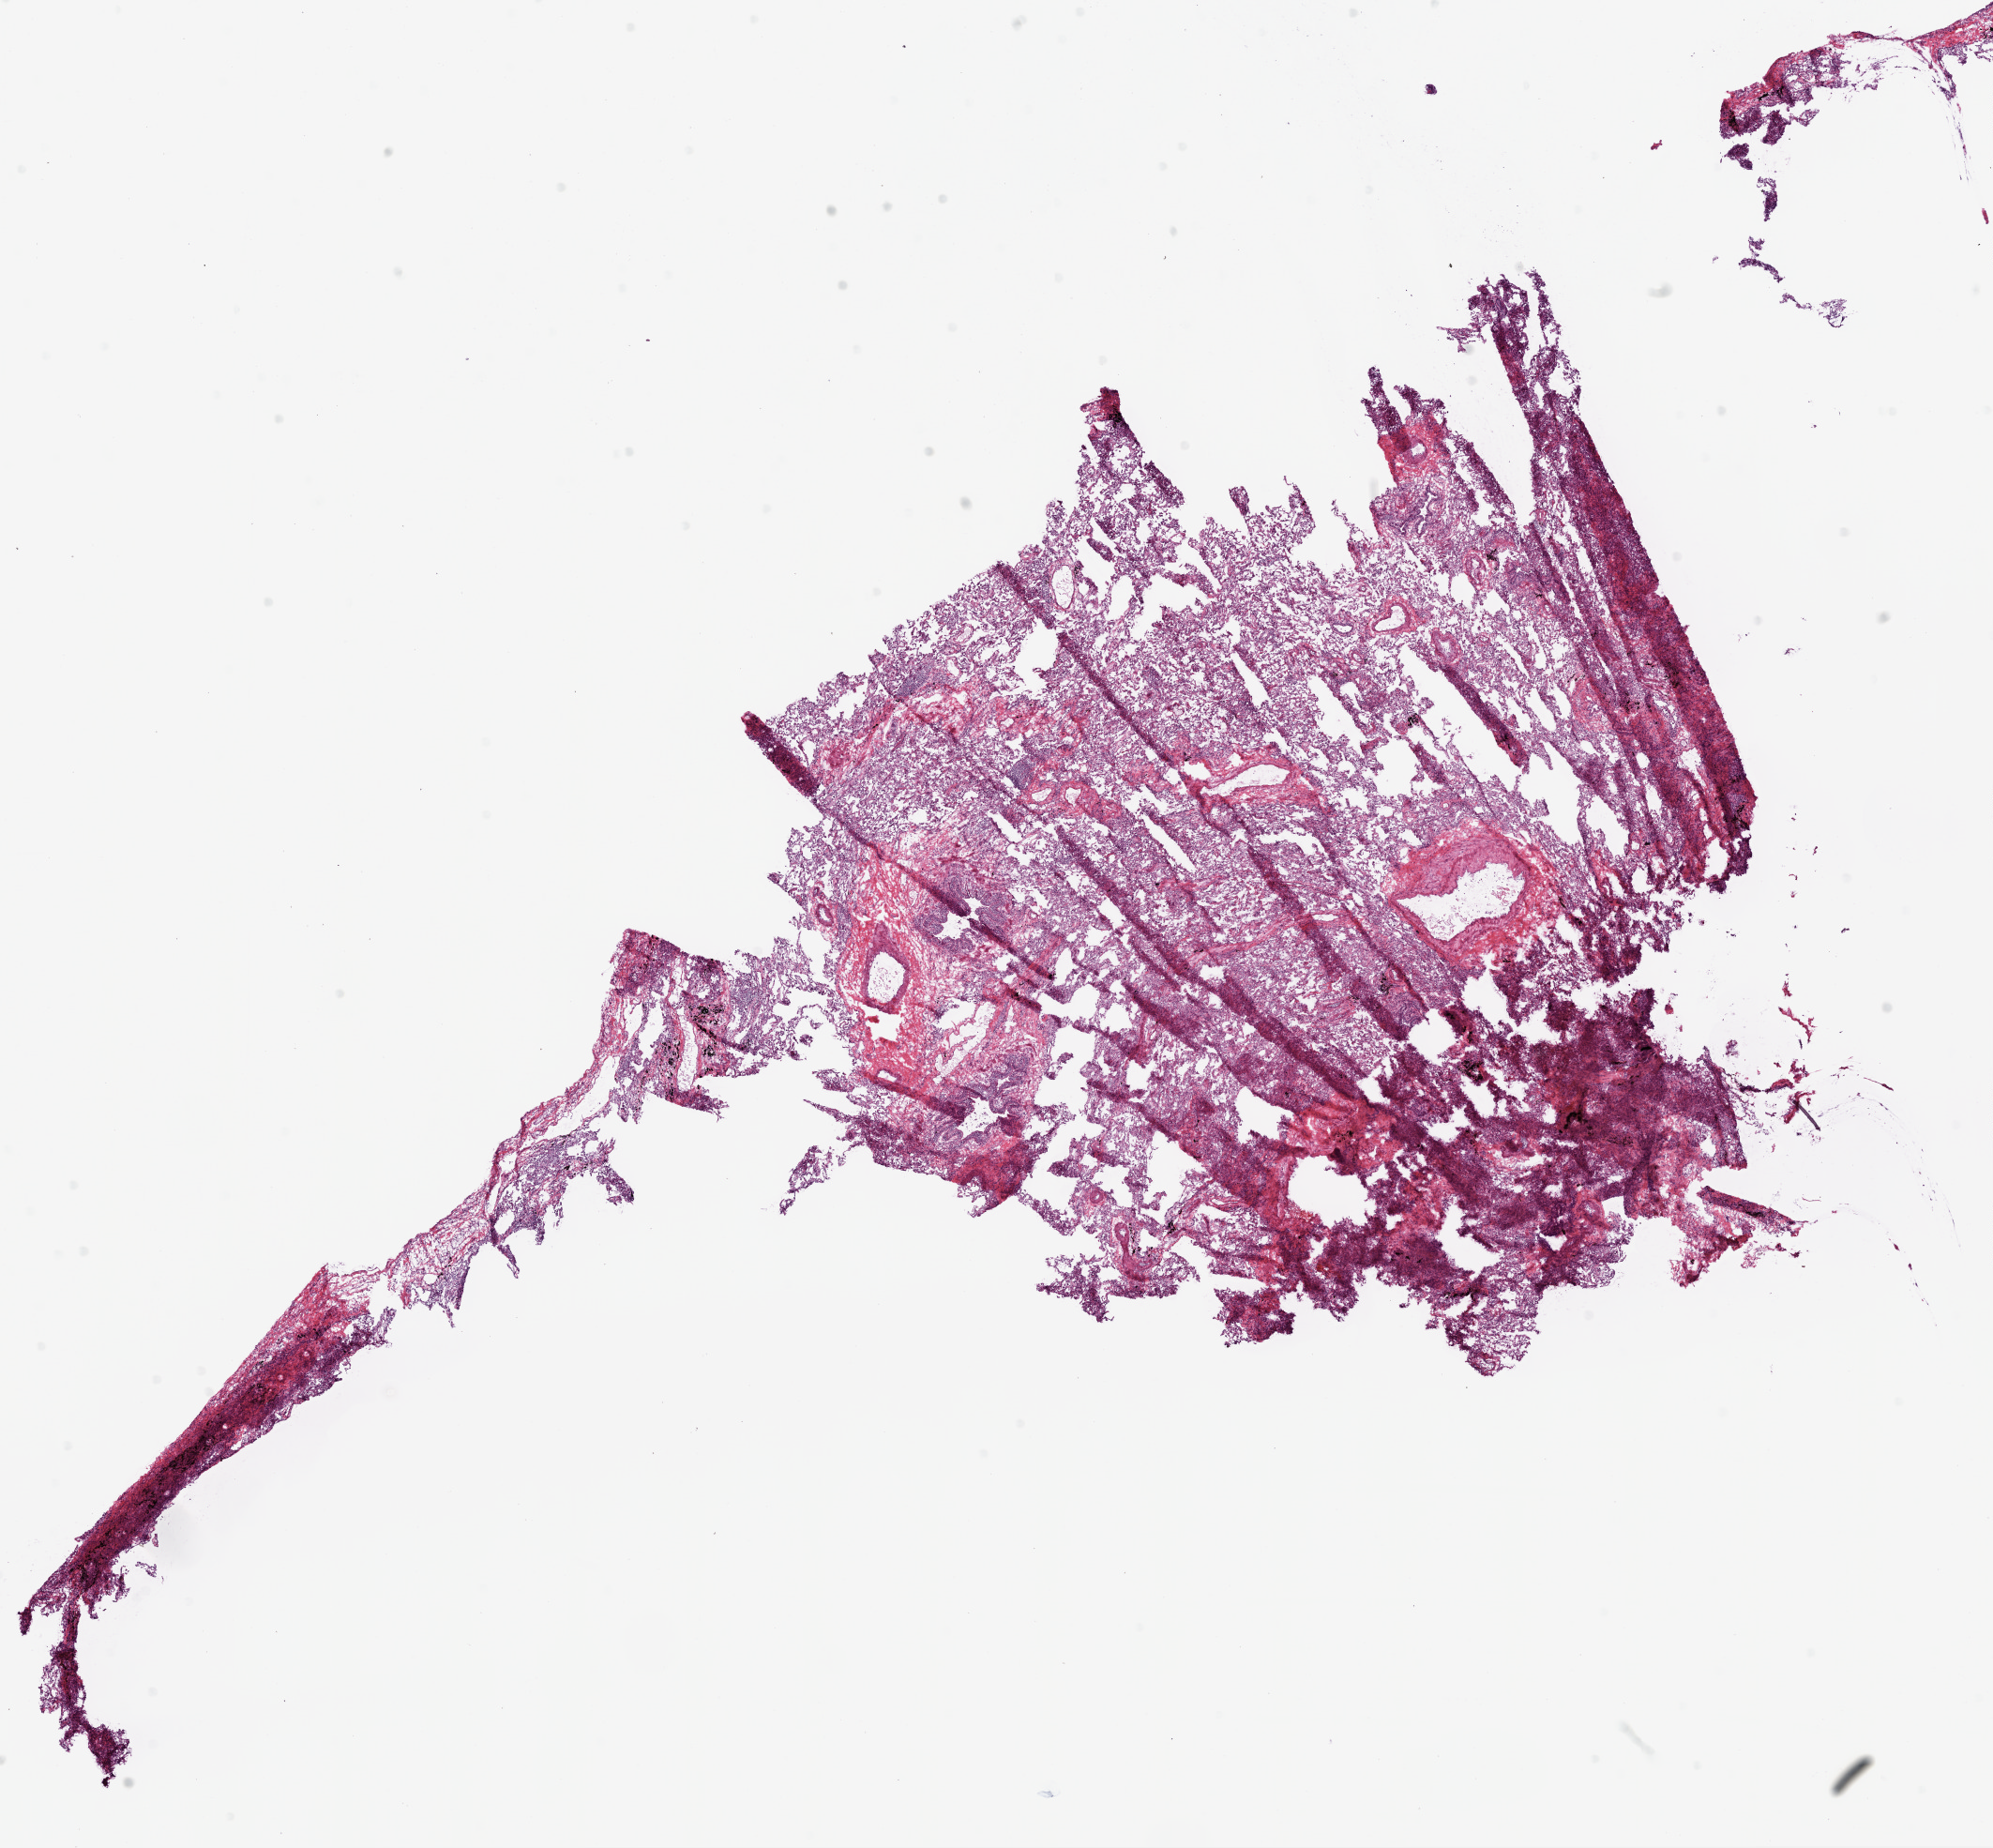
Hematoxylin and eosin (H&E) stained whole-slide image — a low-resolution overview of the entire scanned area, about 17.1 x 15.8 mm (slide scanned at 20x); frozen section; solid tissue normal (non-tumour tissue) sample from the lung. Male patient; age at initial diagnosis 63 years.
This section: solid tissue normal (non-tumour) sample from the same patient. Patient diagnosis: Squamous cell carcinoma, NOS (upper lobe, lung).